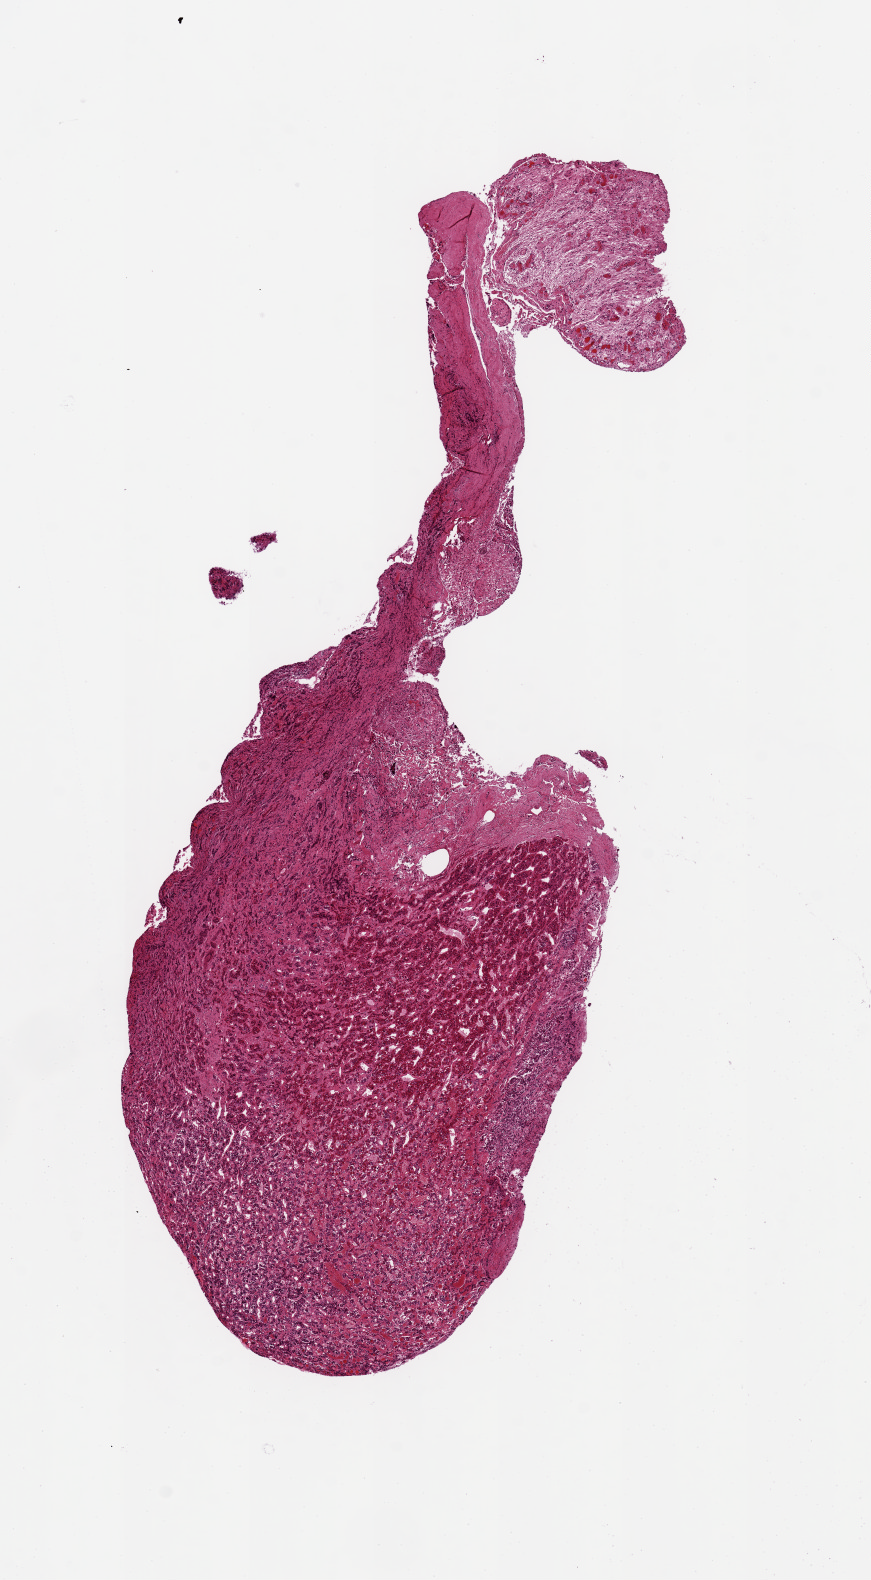
Haematoxylin and eosin whole-slide image — low-resolution overview of the scanned area, about 6.9 x 12.5 mm; PAXgene-fixed paraffin-embedded (PFPE) section; target tissue: pituitary; tissue donor sample. Donor sex: male.
- reviewer comment on this tissue sample: 1 aliquot; ~5x4mm adenohypophysis, attached ~1.5x1.5mm neurohypophysis fragment; Connecting band of fibrous tissue